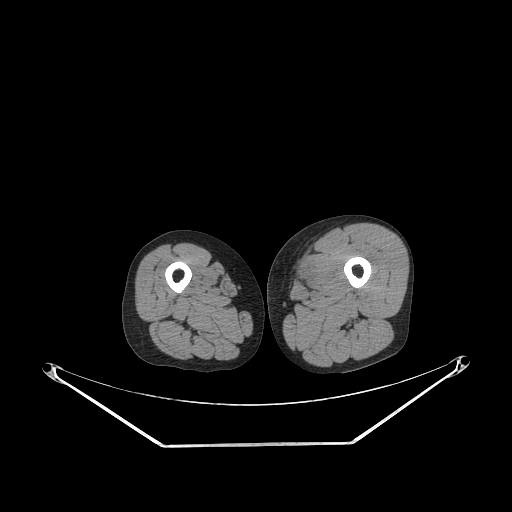
CT of an extremity soft-tissue mass (from a PET/CT study), one axial slice. Soft-tissue window (W 400 / L 40 HU). 3.75 mm slice thickness. 512 × 512 image matrix. Male patient. From the clinical record (not read from this slice): histological type: pleiomorphic leiomyosarcoma; grade: high; site of the primary tumour: left thigh.
Outlined on this slice (expert contour drawn on MRI and transferred to this co-registered scan by the dataset authors):
- gross tumour volume including surrounding oedema: bounding box (x1, y1, x2, y2) in pixels: (290, 258, 314, 289)